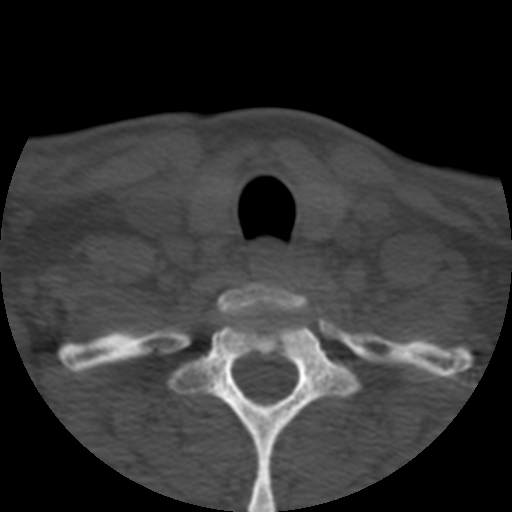
CT including the spine, one axial slice; slice 451 of 508 in the series (ordered by position); reconstruction kernel STANDARD; 120 kVp; bone window (W 1800 / L 400 HU); 1.25 mm slice thickness; 512 × 512 image matrix, field of view 160 × 160 mm. Patient age 57 years. From the clinical record (not read from this slice): primary cancer: prostate.
Structures marked on this image (semi-automatically segmented with operator editing):
- T1 vertebra: bounding box (x1, y1, x2, y2) in pixels: (170, 305, 358, 512)